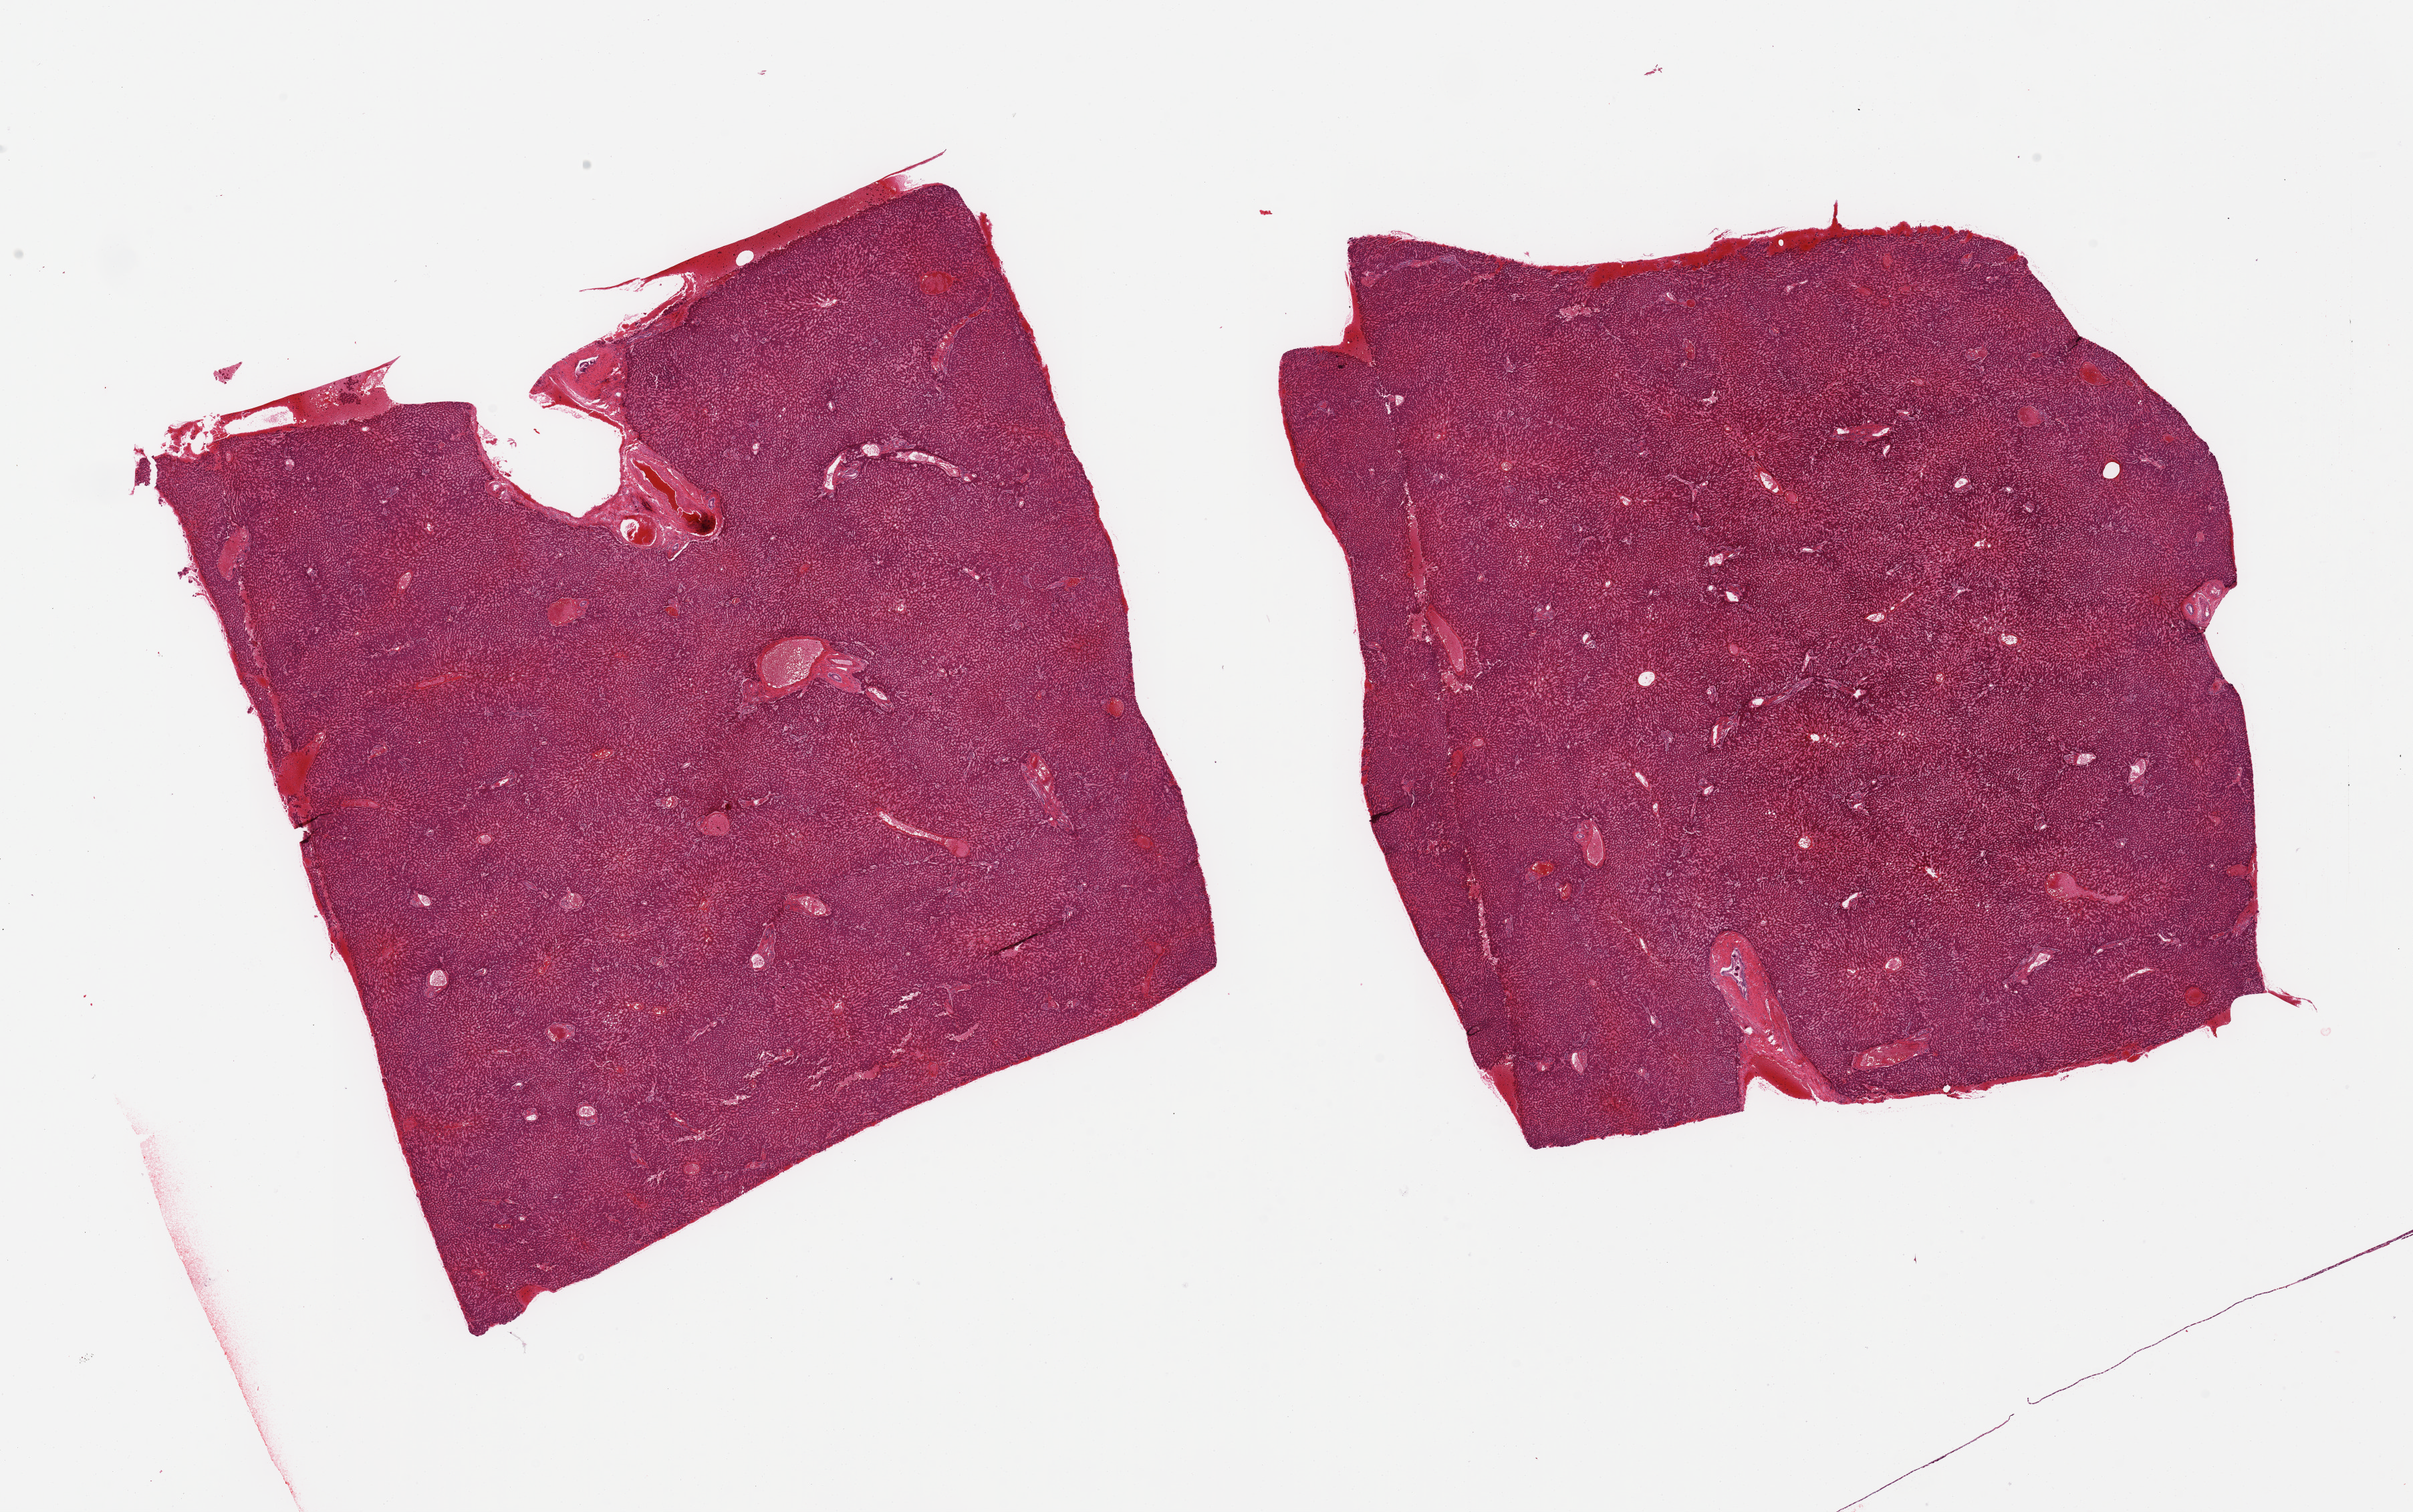
Digitized H&E-stained section — low-resolution overview of the scanned area, about 28.5 x 17.9 mm; PAXgene-fixed, paraffin-embedded tissue; section of liver (target tissue); donor tissue sample. Donor sex: female.
Pathologist's review note for this sample: 2 pieces, moderate passive congestion.